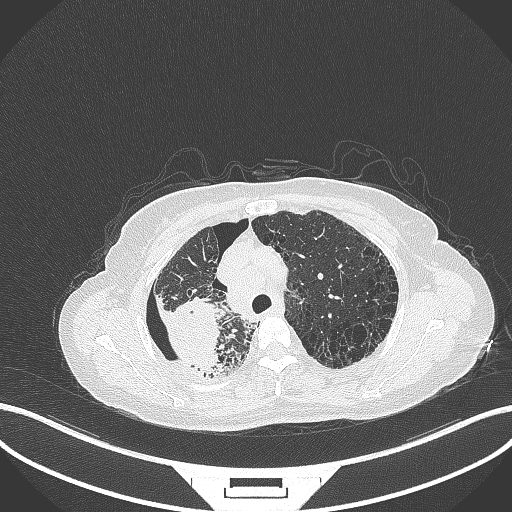
Chest CT, one axial slice. Slice 268 of 408 in the series (ordered by position). Reconstruction kernel B70f. Lung window (W 1500 / L -600 HU). 1 mm slice thickness. 512 × 512 image matrix. Patient: female, 64 years. From the clinical record (not read from this slice): clinical TNM (as recorded): T3 N3 M0.
Outlined on this slice (bounding box drawn by a radiologist):
- lung tumour (recorded histology: squamous cell carcinoma): bounding box <154,290,224,374> (left, top, right, bottom; pixels)